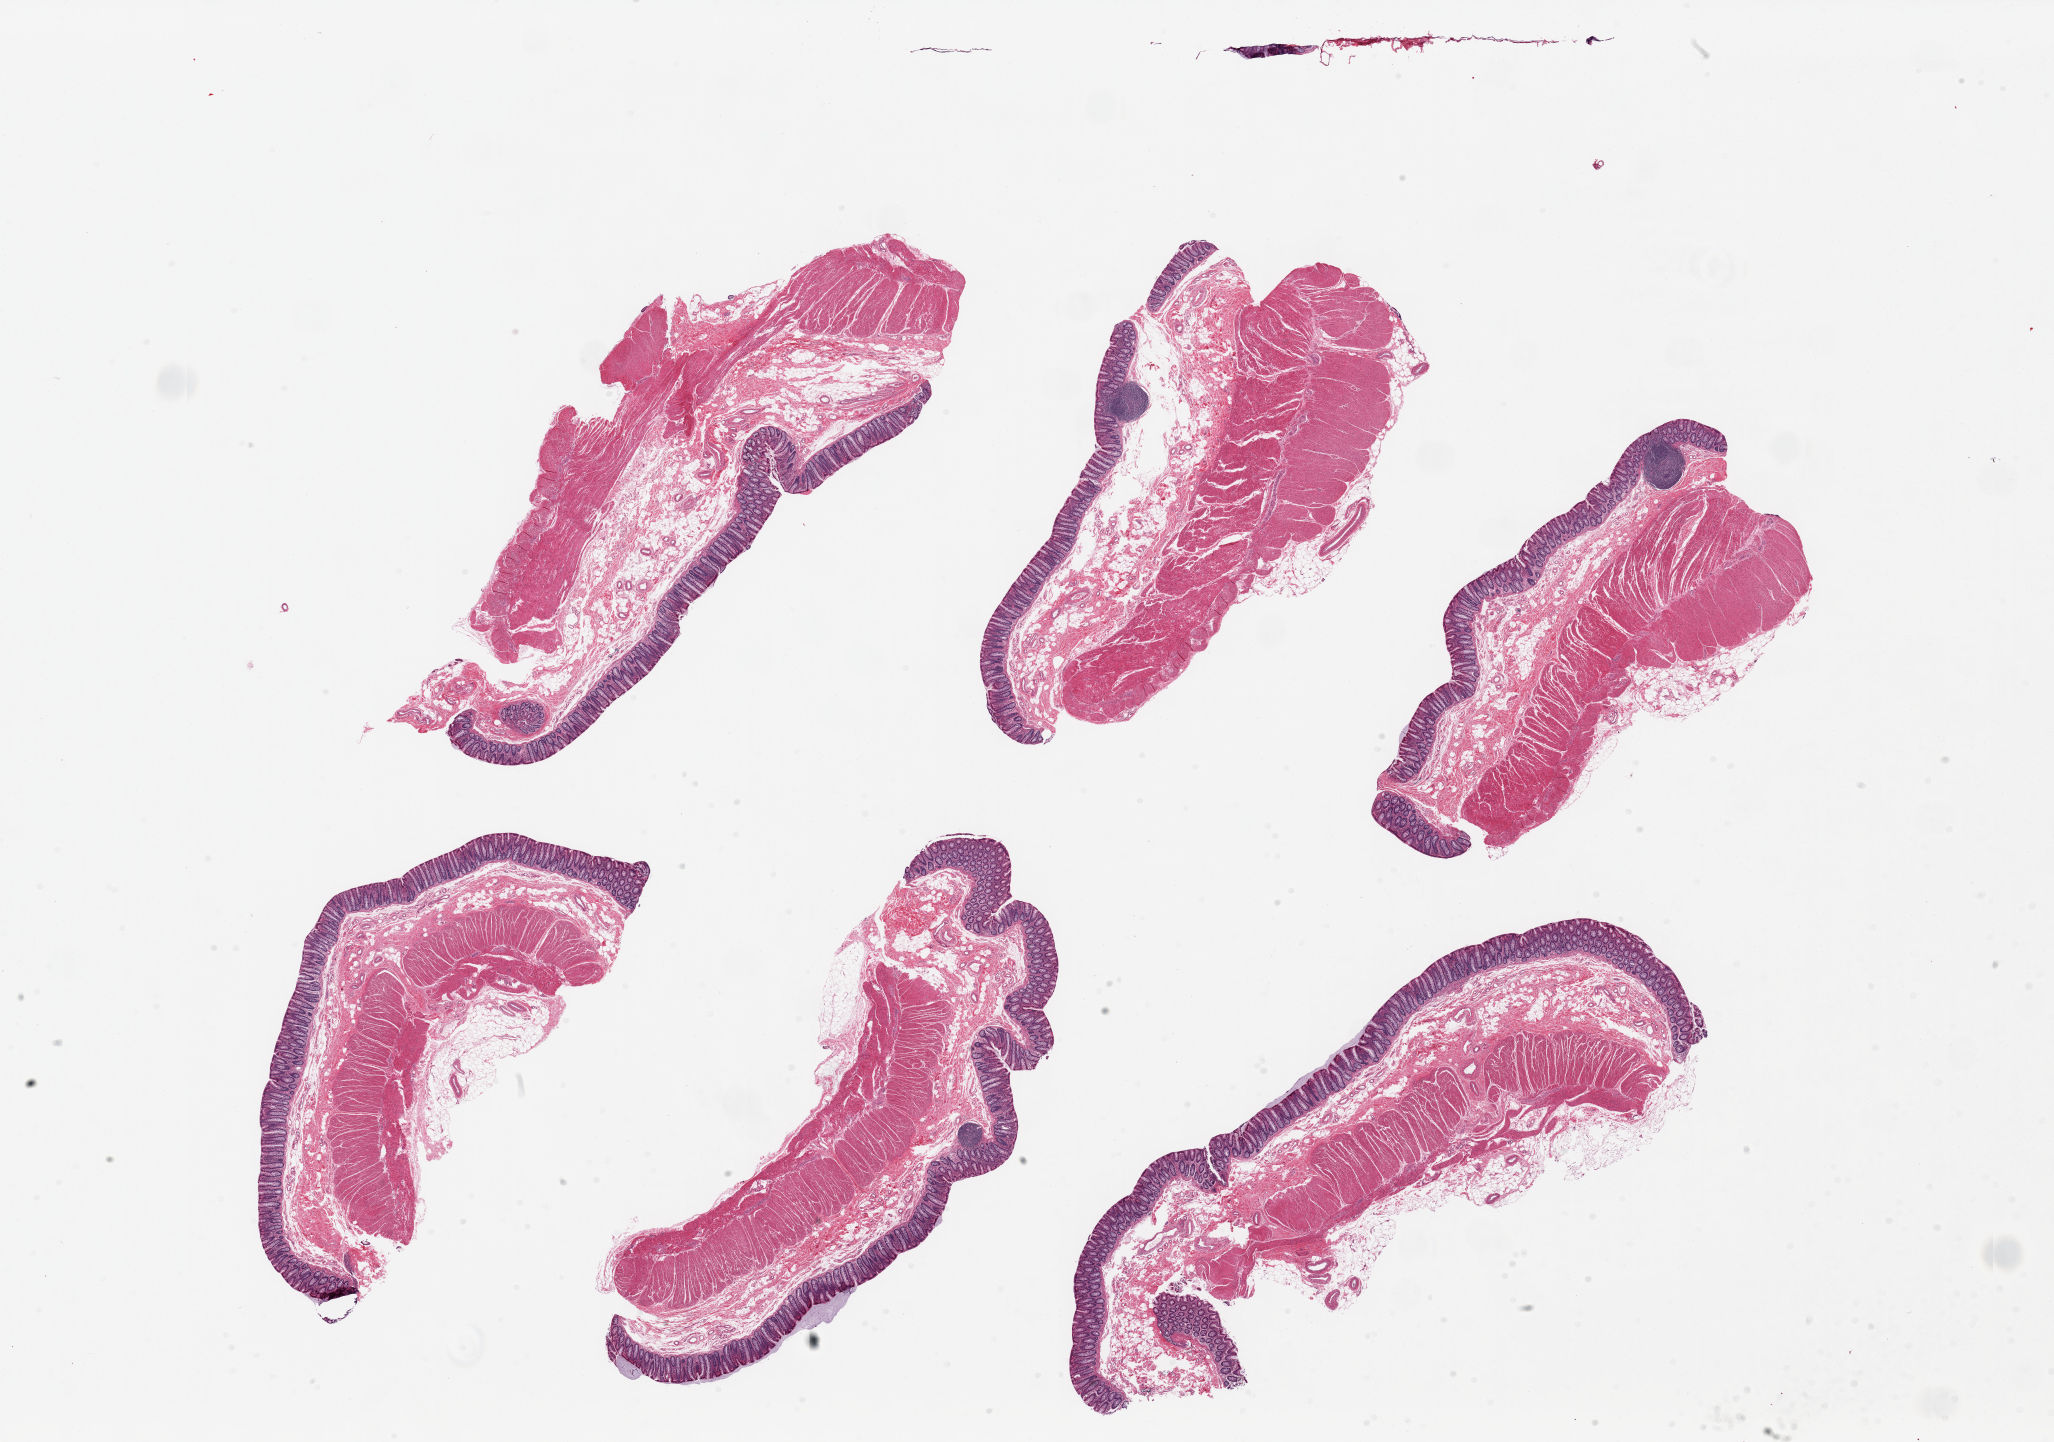
Whole-slide image, hematoxylin and eosin (H&E) stain, brightfield, low-resolution overview of the scanned area, about 32.5 x 22.8 mm (from a 20x scan). PAXgene-fixed, paraffin-embedded tissue. Sampled site (target tissue): transverse colon. Tissue donor sample. Donor: male.
- pathologist's review note for this sample: 6 pieces, target mucosa up to ~0.5mm, ~10-15% thickness